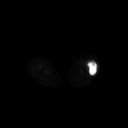
FDG PET of an extremity soft-tissue mass (from a PET/CT study), one axial slice; position 206 of 267 along the scan axis; 3.27 mm slice thickness; 128 × 128 image matrix. Female patient, age 62 years. Case-level facts recorded for this patient, not image findings: histological type: undifferentiated – high grade; grade: high; site of the primary tumour: left thigh.
Structures marked on this image (expert contour drawn on MRI and transferred to this co-registered scan by the dataset authors):
- gross tumour volume including surrounding oedema: bounding box <84,60,97,75> (left, top, right, bottom; pixels)
- gross tumour volume (mass): <87,60,97,75>